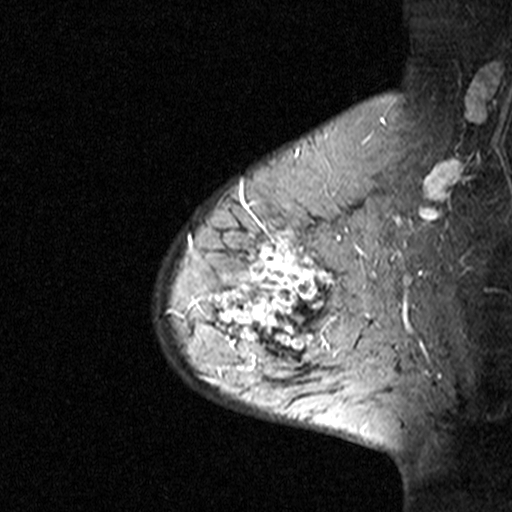
Breast MRI (dynamic contrast-enhanced), one sagittal slice. Slice 32 of 44 in the series (ordered by position). Dynamic contrast-enhanced study with each time point stored as its own series, time point 3 of 4 at this slice position (ordered by acquisition time). 1.5 T. TE 4.5 ms, TR 11 ms. 3 mm slice thickness. 512 × 512 image matrix, field of view 200 × 200 mm. Female patient, age 65 years. From the clinical record (not read from this slice): setting: breast cancer imaged before/during neoadjuvant chemotherapy; receptor status: HER2-positive.
Structures marked on this image (semi-automatic segmentation, software-assisted and operator-edited):
- analysis volume of interest (the breast-tissue region the enhancement analysis was run in; not a lesion): bounding box <182,190,353,361> (left, top, right, bottom; pixels)
- tumour enhancement mask (voxels above the 90 % enhancement threshold inside the analysis volume of interest): <188,226,336,350>